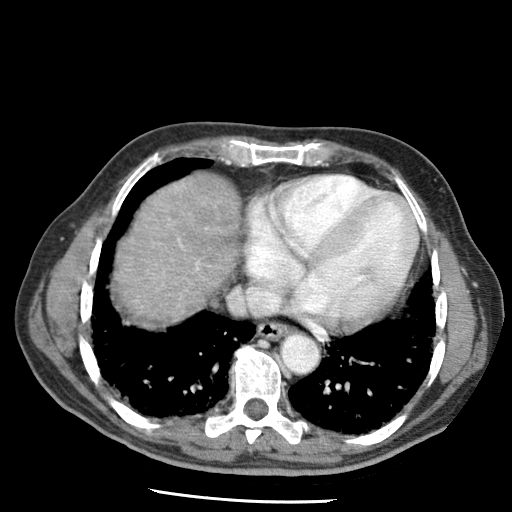
Contrast-enhanced abdominal CT (liver protocol), one axial slice; slice 63 of 79 in the series (ordered by position); reconstruction kernel STANDARD; 120 kVp; soft-tissue window (W 400 / L 40 HU); 512 × 512 image matrix. Case-level facts recorded for this patient, not image findings: diagnosis: hepatocellular carcinoma (patient treated with transarterial chemoembolisation; whether this scan precedes or follows treatment is not stated here); TNM stage (as recorded): Stage-IIIA; Child-Pugh class: A; tumour differentiation: moderately differentiated; tumour nodularity: multinodular.
Outlined on this slice (semi-automatic segmentation, software-assisted and operator-edited):
- liver parenchyma outside the tumour (the mass and vessels are separate outlines, so this box may not span the whole liver): box from (x=114, y=176) to (x=240, y=324) px
- liver vessels: (x=169, y=187)–(x=200, y=271)